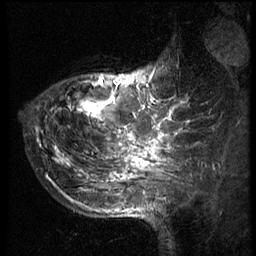
Breast MRI (dynamic contrast-enhanced), one sagittal slice. Slice 20 of 66 in the series (ordered by position). 3 images stored at this slice position (order not interpretable as contrast timing). 1.5 T. TE 4.2 ms, TR 8.9 ms. 2.5 mm slice thickness. 256 × 256 image matrix. Female patient, age 39 years. Case-level facts recorded for this patient, not image findings: setting: breast cancer imaged before/during neoadjuvant chemotherapy; receptor status: HER2-positive.
Annotated regions visible in this slice (semi-automatic segmentation, software-assisted and operator-edited):
- analysis volume of interest (the breast-tissue region the enhancement analysis was run in; not a lesion): bounding box [x1, y1, x2, y2] px = [29, 48, 166, 196]
- tumour enhancement mask (voxels above the 140 % enhancement threshold inside the analysis volume of interest): [54, 75, 166, 182]